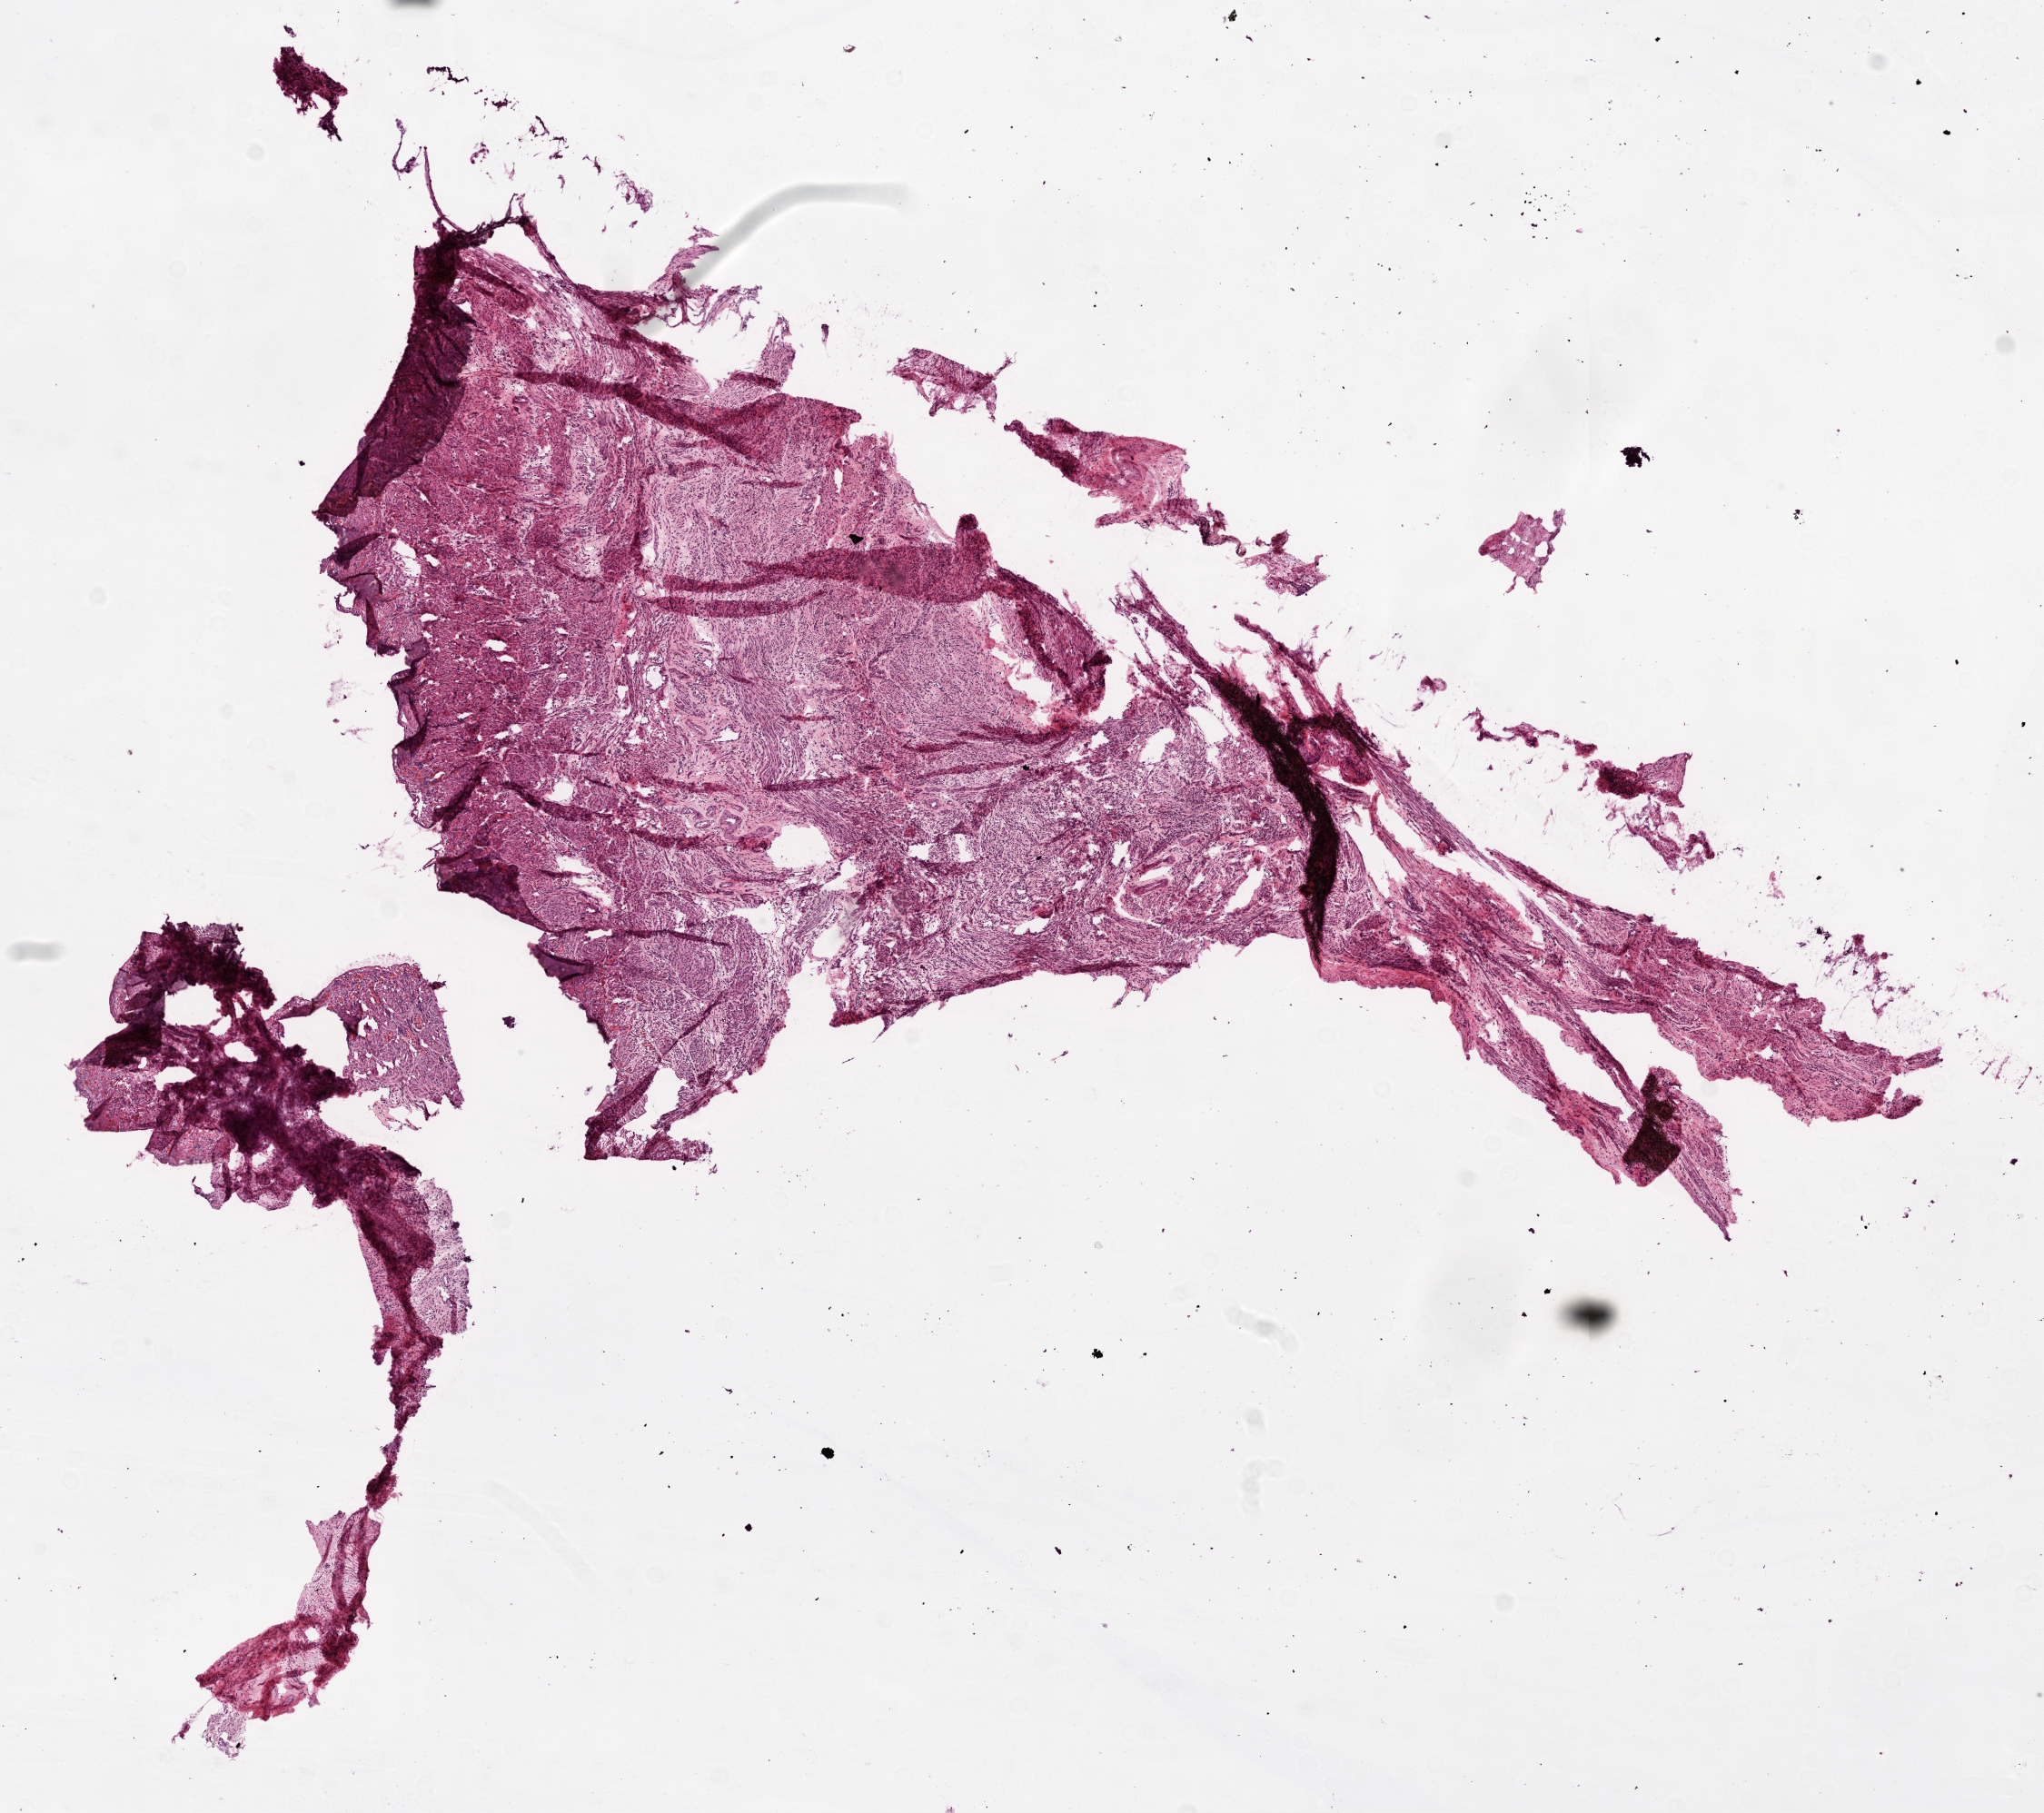
Hematoxylin and eosin (H&E) stained whole-slide image — shown as a low-resolution overview of the whole scanned area (about 9.0 x 8.0 mm, acquisition: 20x scan). Frozen section. Ovary, solid tissue normal (non-tumour tissue) sample. Female patient; age at initial diagnosis 63 years.
This section: solid tissue normal sample (biorepository sample class). Patient diagnosis: Serous cystadenocarcinoma, NOS.